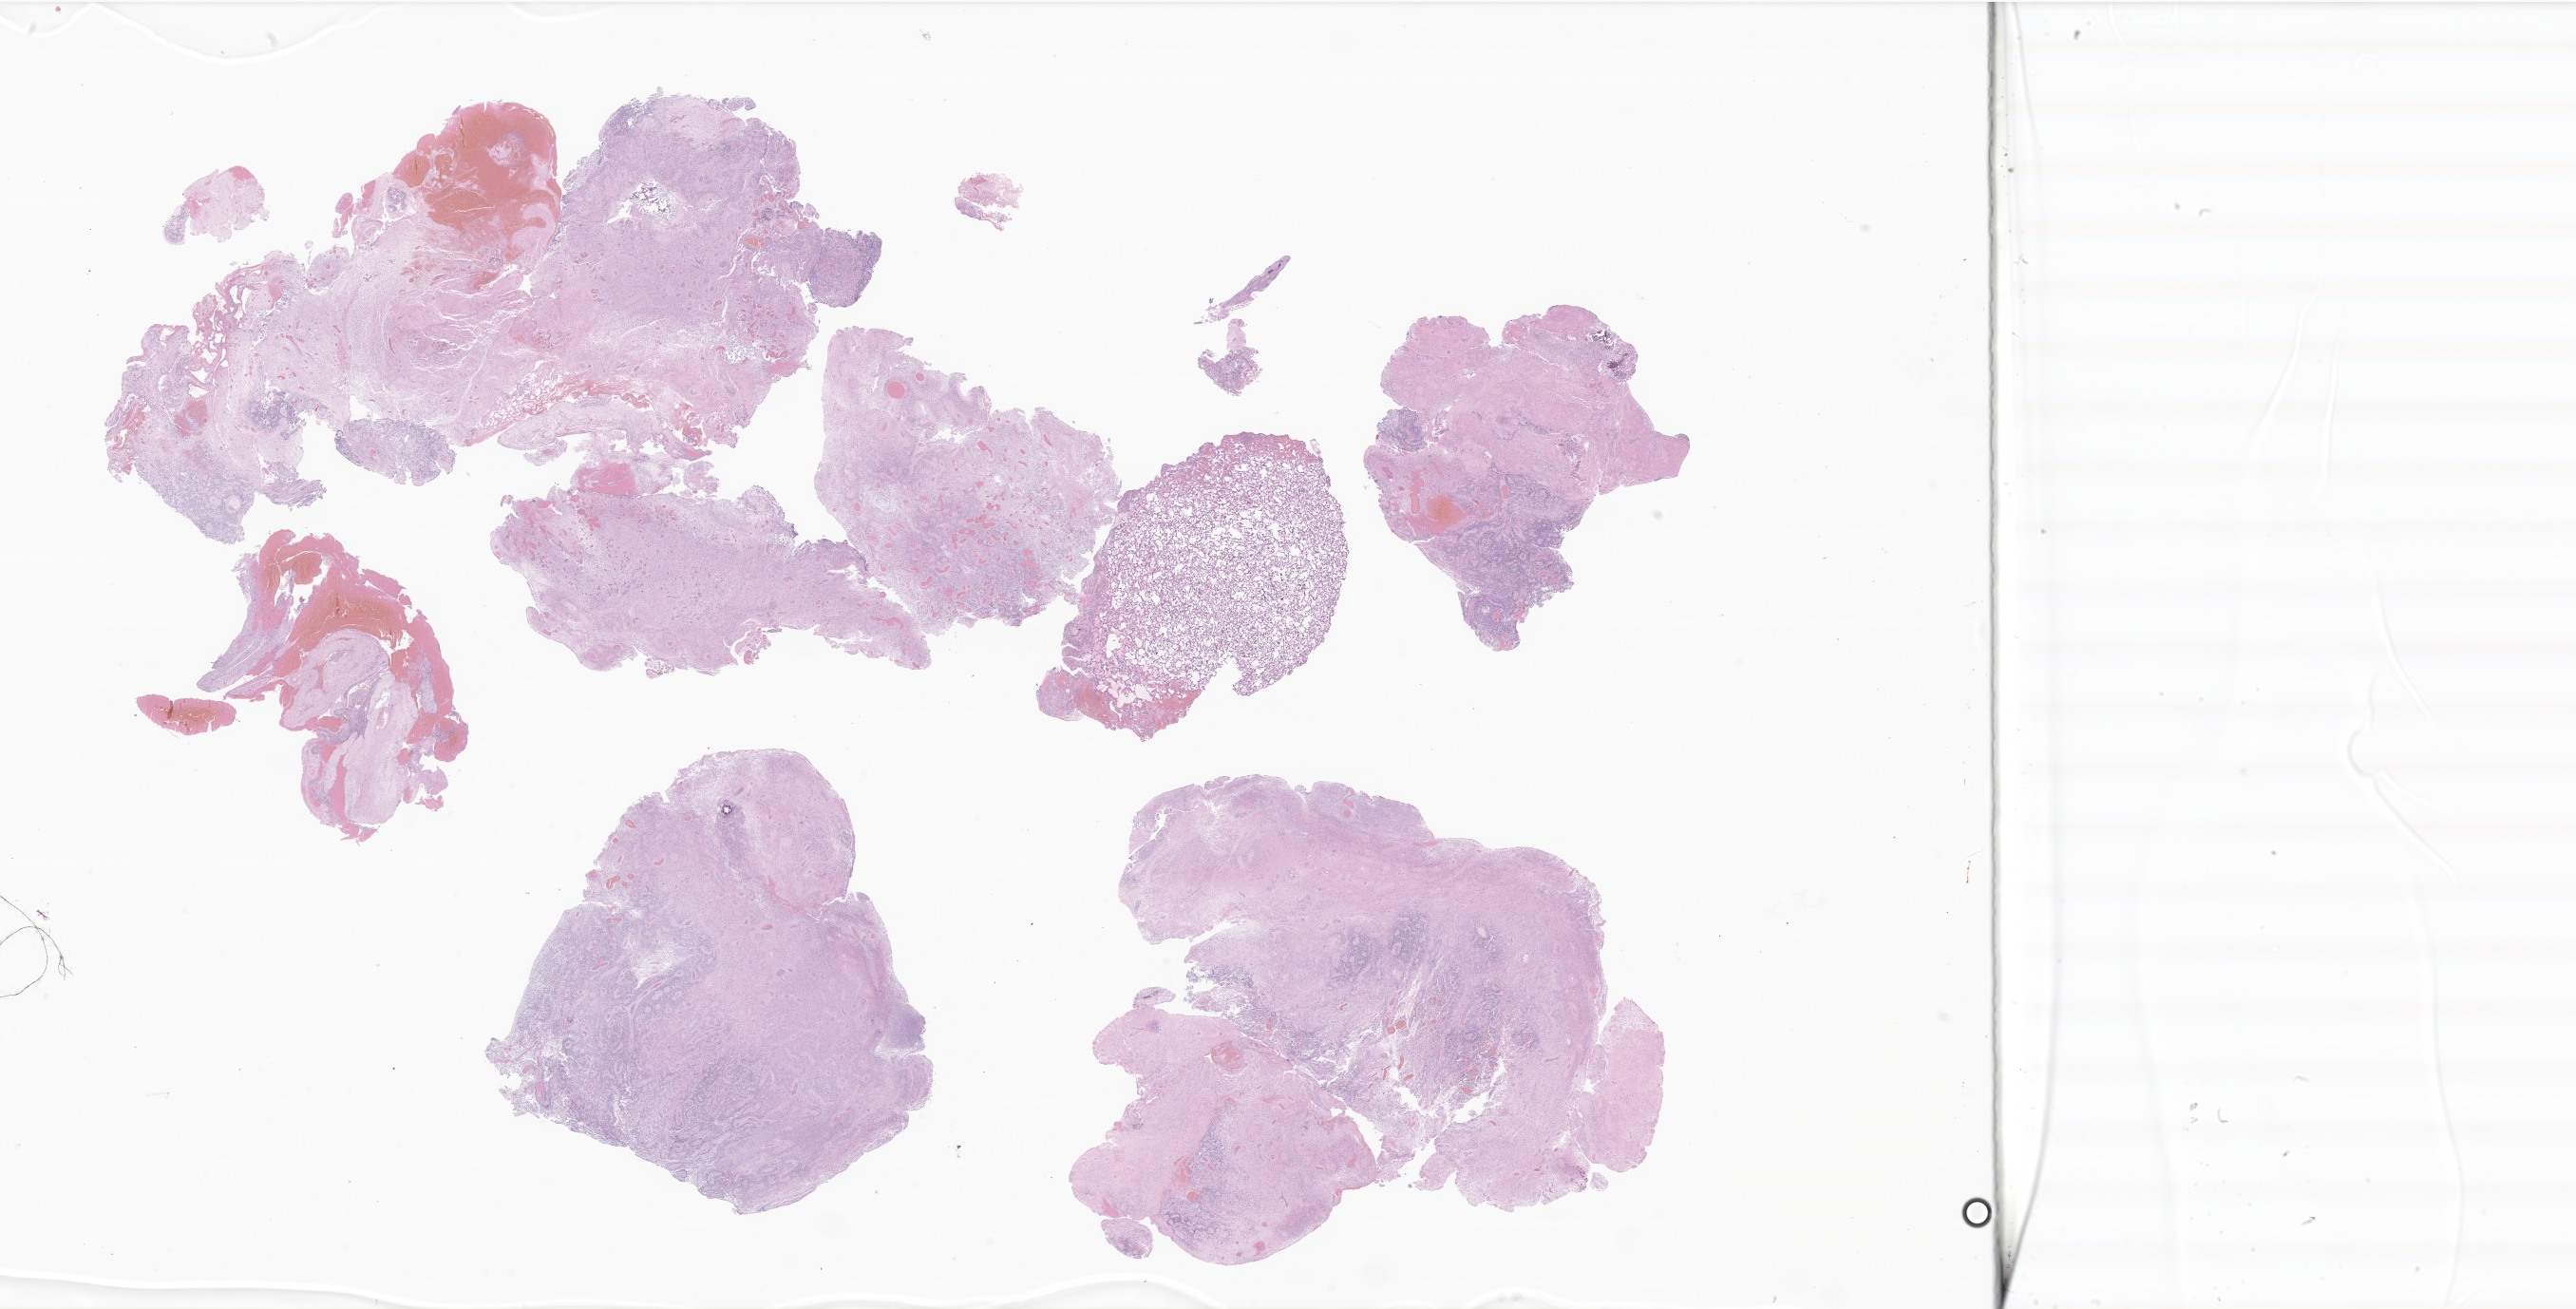
Hematoxylin and eosin (H&E) whole-slide image of tumor tissue from the brain — a low-resolution overview of the entire scanned area, about 45.7 x 23.2 mm, FFPE section. Patient male; age 525 days.
Diagnosis: Ependymoma, anaplastic.